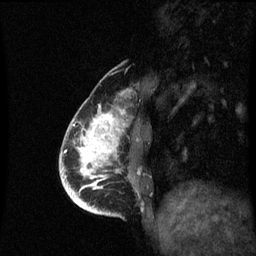
Breast MRI (dynamic contrast-enhanced), one sagittal slice; slice 19 of 60 in the series (ordered by position); dynamic contrast-enhanced series, image 2 of 3 at this slice position (ordered by acquisition); 1.5 T; TE 4.2 ms, TR 8.9 ms; 2 mm slice thickness; 256 × 256 image matrix, field of view 200 × 200 mm. Female patient, age 35 years. Case-level facts recorded for this patient, not image findings: setting: breast cancer imaged before/during neoadjuvant chemotherapy; receptor status: HR-positive, HER2-negative.
Outlined on this slice (semi-automatically segmented with operator editing):
- analysis volume of interest (the breast-tissue region the enhancement analysis was run in; not a lesion): bounding box <66,100,131,215> (left, top, right, bottom; pixels)
- tumour enhancement mask (voxels above the 70 % enhancement threshold inside the analysis volume of interest): <69,114,120,213>